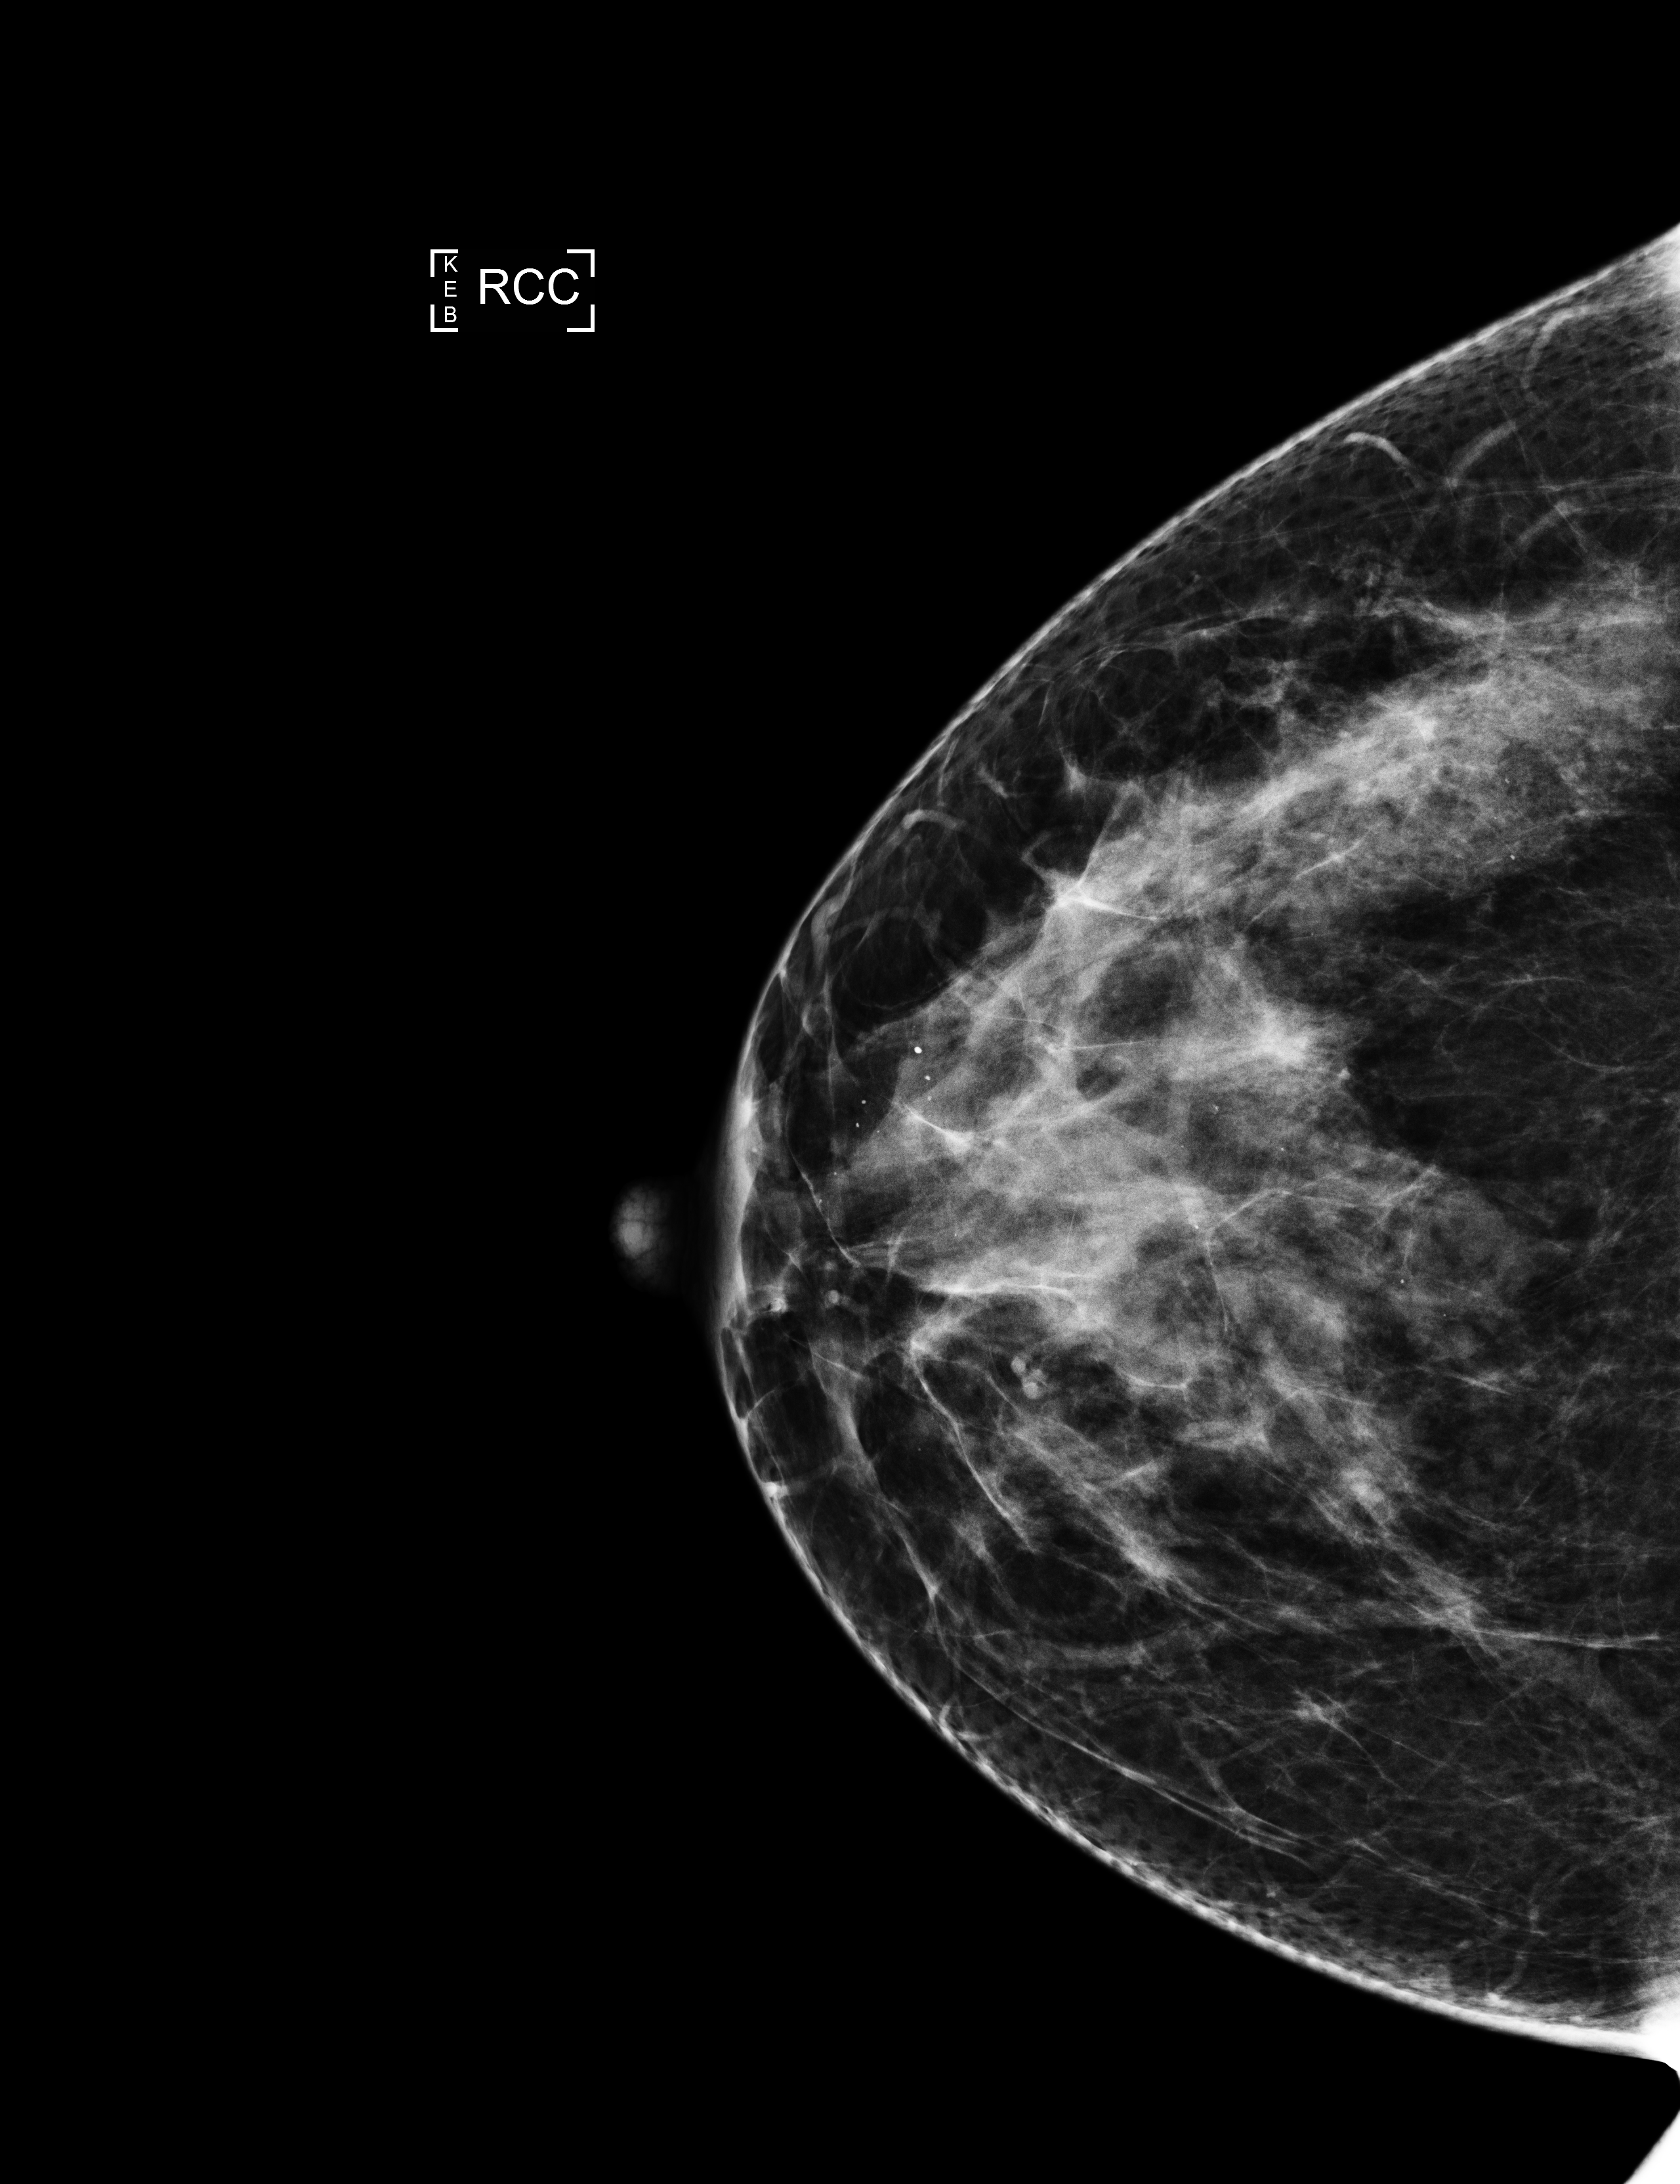
Annual screening mammography examination. Female patient, age 41 years.
Image type: full-field digital mammogram. Breast: right. Projection: cranio-caudal projection.